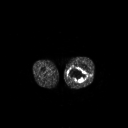
FDG PET of an extremity soft-tissue mass (from a PET/CT study), one axial slice; position 227 of 267 along the scan axis; 3.27 mm slice thickness; 128 × 128 image matrix. Patient: male, 44 years. Case-level facts recorded for this patient, not image findings: histological type: undifferentiated pleomorphic liposarcoma; grade: high; site of the primary tumour: left thigh.
Structures marked on this image (expert contour drawn on MRI and transferred to this co-registered scan by the dataset authors):
- gross tumour volume including surrounding oedema: box from (x=67, y=67) to (x=87, y=83) px
- gross tumour volume (mass): (x=67, y=67)–(x=87, y=83)